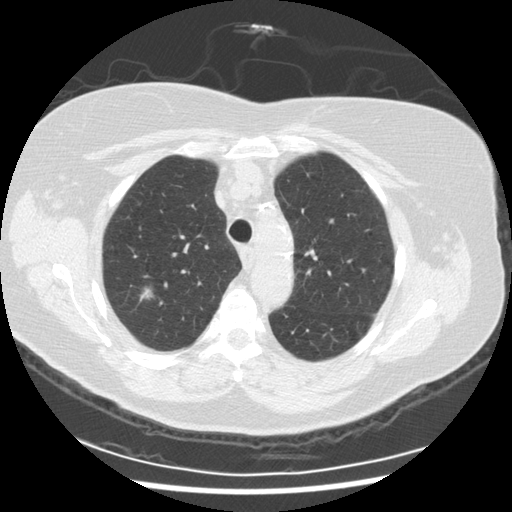
Low-dose screening chest CT, one axial slice; slice 200 of 254 in the series (ordered by position); reconstruction kernel STANDARD; 120 kVp; lung window (W 1500 / L -600 HU); 2.5 mm slice thickness; 512 × 512 image matrix.
Annotated regions visible in this slice (manually delineated by an expert):
- lesion 1 (tumor, upper lobe of right lung): bounding box <140,288,153,302> (left, top, right, bottom; pixels)